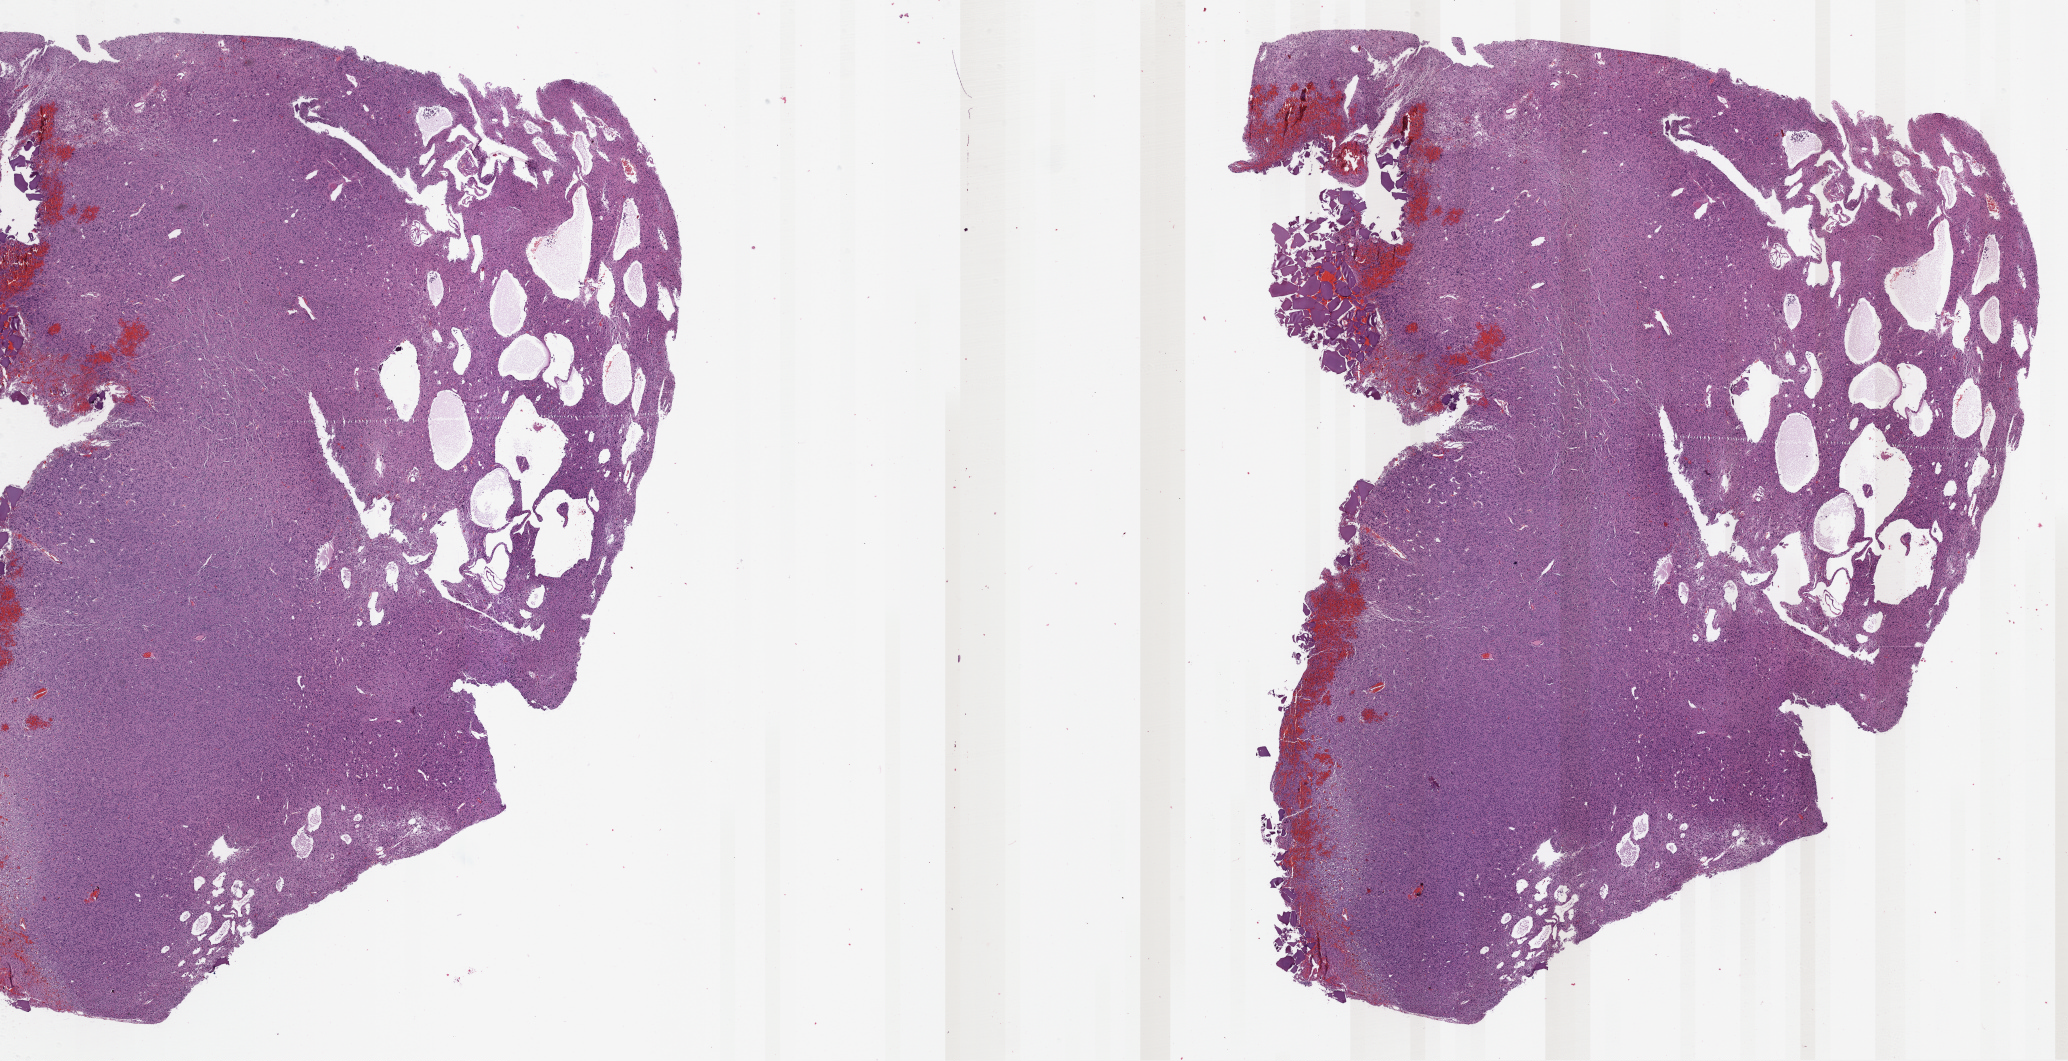
Digitized H&E-stained tissue section (whole slide), shown as a low-resolution overview of the whole scanned area (about 33.4 x 17.1 mm), formalin-fixed paraffin-embedded (FFPE) diagnostic section, primary tumour sample from the brain. Male patient; age at initial diagnosis 37 years. Histologic grade: G3 (poorly differentiated).
• laterality: right
• histologic diagnosis: Astrocytoma, anaplastic (cerebrum)